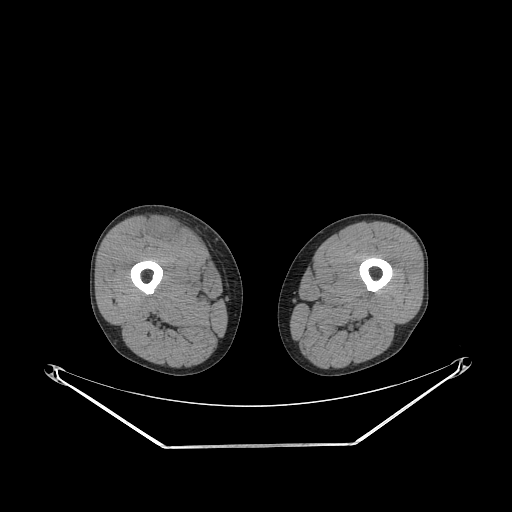
CT of an extremity soft-tissue mass (from a PET/CT study), one axial slice; slice 244 of 311 in the series (ordered by position); soft-tissue window (W 400 / L 40 HU); 512 × 512 image matrix, field of view 500 × 500 mm. Male patient. Case-level facts recorded for this patient, not image findings: histological type: pleiomorphic leiomyosarcoma; grade: intermediate; site of the primary tumour: right thigh.
Structures marked on this image (expert contour drawn on MRI and transferred to this co-registered scan by the dataset authors):
- gross tumour volume including surrounding oedema: box from (x=148, y=219) to (x=181, y=243) px